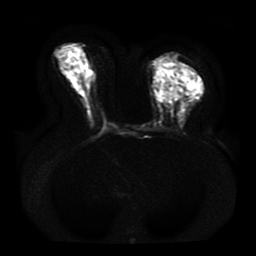
Breast MRI, one axial slice. Slice 20 of 41 in the series (ordered by position). Diffusion-weighted series; image 2 of 4 stored at this slice position (different b-values; order by instance number). 1.5 T. 256 × 256 image matrix, field of view 330 × 330 mm. Female patient.
Annotated regions visible in this slice (expert manual segmentation):
- tumour on diffusion-weighted imaging: box from (x=169, y=80) to (x=201, y=98) px